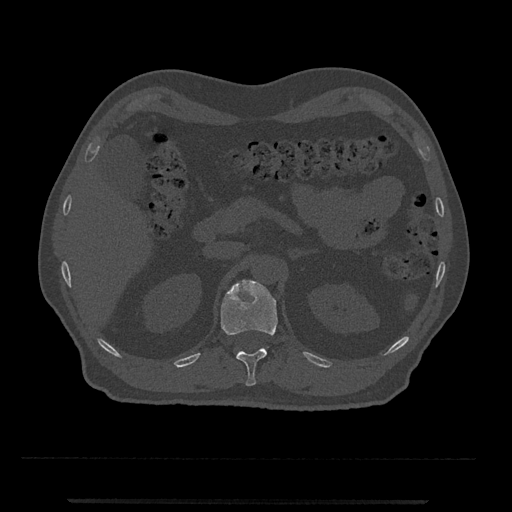
CT including the spine, one axial slice. Slice 387 of 797 in the series (ordered by position). Reconstruction kernel Br40s/3. 120 kVp. Bone window (W 1800 / L 400 HU). 0.5 mm slice thickness. 512 × 512 image matrix, field of view 419 × 419 mm. Male patient, age 63 years. From the clinical record (not read from this slice): primary cancer: prostate.
Outlined on this slice (semi-automatic segmentation, software-assisted and operator-edited):
- T12 vertebra: bounding box <220,279,278,386> (left, top, right, bottom; pixels)